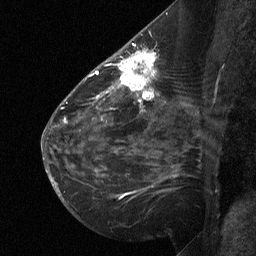
Breast MRI (dynamic contrast-enhanced), one sagittal slice. Position 36 of 64 along the scan axis. Dynamic contrast-enhanced study with each time point stored as its own series, time point 2 of 3 at this slice position (early post-contrast, ordered by acquisition time). 1.5 T. TE 4.8 ms, TR 27 ms. 256 × 256 image matrix, field of view 200 × 200 mm. Female patient, age 51 years. From the clinical record (not read from this slice): setting: breast cancer imaged before/during neoadjuvant chemotherapy; receptor status: HR-positive, HER2-negative.
Structures marked on this image (semi-automatic segmentation, software-assisted and operator-edited):
- analysis volume of interest (the breast-tissue region the enhancement analysis was run in; not a lesion): box from (x=112, y=46) to (x=169, y=106) px
- tumour enhancement mask (voxels above the 90 % enhancement threshold inside the analysis volume of interest): (x=112, y=50)–(x=155, y=102)